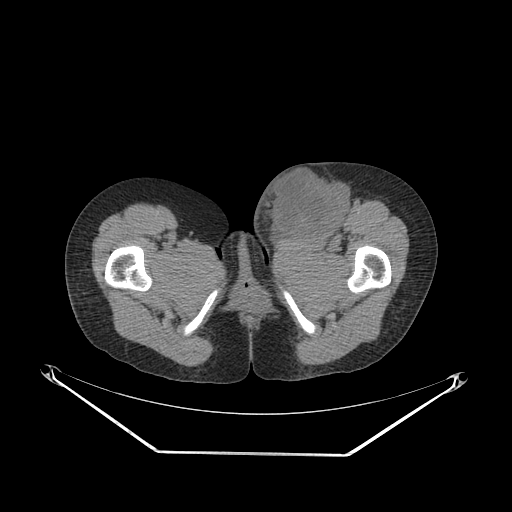
CT of an extremity soft-tissue mass (from a PET/CT study), one axial slice. Position 52 of 267 along the scan axis. Reconstruction kernel SOFT. 140 kVp. Soft-tissue window (W 400 / L 40 HU). 512 × 512 image matrix, field of view 500 × 500 mm. Female patient. Case-level facts recorded for this patient, not image findings: histological type: leiomyosarcoma; grade: high; site of the primary tumour: groin.
Outlined on this slice (expert contour drawn on MRI and transferred to this co-registered scan by the dataset authors):
- gross tumour volume including surrounding oedema: bounding box <251,160,350,243> (left, top, right, bottom; pixels)
- gross tumour volume (mass): <272,167,348,239>